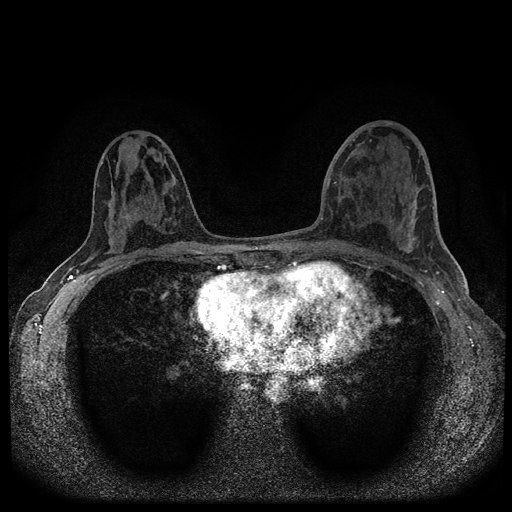
Breast MRI (dynamic contrast-enhanced, multi-phase), one axial slice. Slice 55 of 116 in the series (ordered by position). Dynamic contrast-enhanced series, time point 2 of 5 at this slice position (early post-contrast). 1.5 T. TE 2.7 ms, TR 5.6 ms. 2 mm slice thickness. 512 × 512 image matrix. Female patient, age 40 years.
Outlined on this slice (semi-automatic segmentation, software-assisted and operator-edited):
- breast lesion (labelled benign in the annotation): box from (x=123, y=205) to (x=131, y=220) px